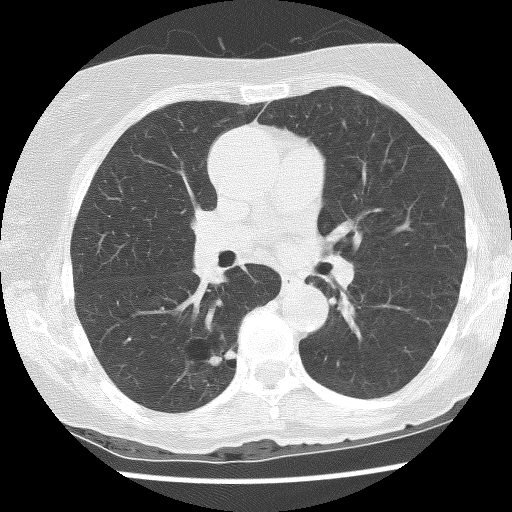
Axial slice from a low-dose chest CT screening exam; baseline annual screen; lung window (W 1500 / L -600 HU); 2.5 mm slice thickness; lung (sharp) reconstruction kernel (BONE); 512 × 512 image matrix. Female, age 69 years at enrolment. Former smoker at enrolment.
Expert reader's lesion annotation, bounding box [x1, y1, x2, y2] px = [152, 318, 249, 395]. The screening reader recorded 2 non-calcified nodules or masses ≥4 mm on this exam (right lower lobe, right lower lobe); which of them this box marks is not recorded. Participant outcome: lung cancer diagnosed 288 days after this screen — non-small cell carcinoma, right lower lobe, poorly differentiated (G3), stage IB (AJCC 6th edition), 36 mm at pathology.